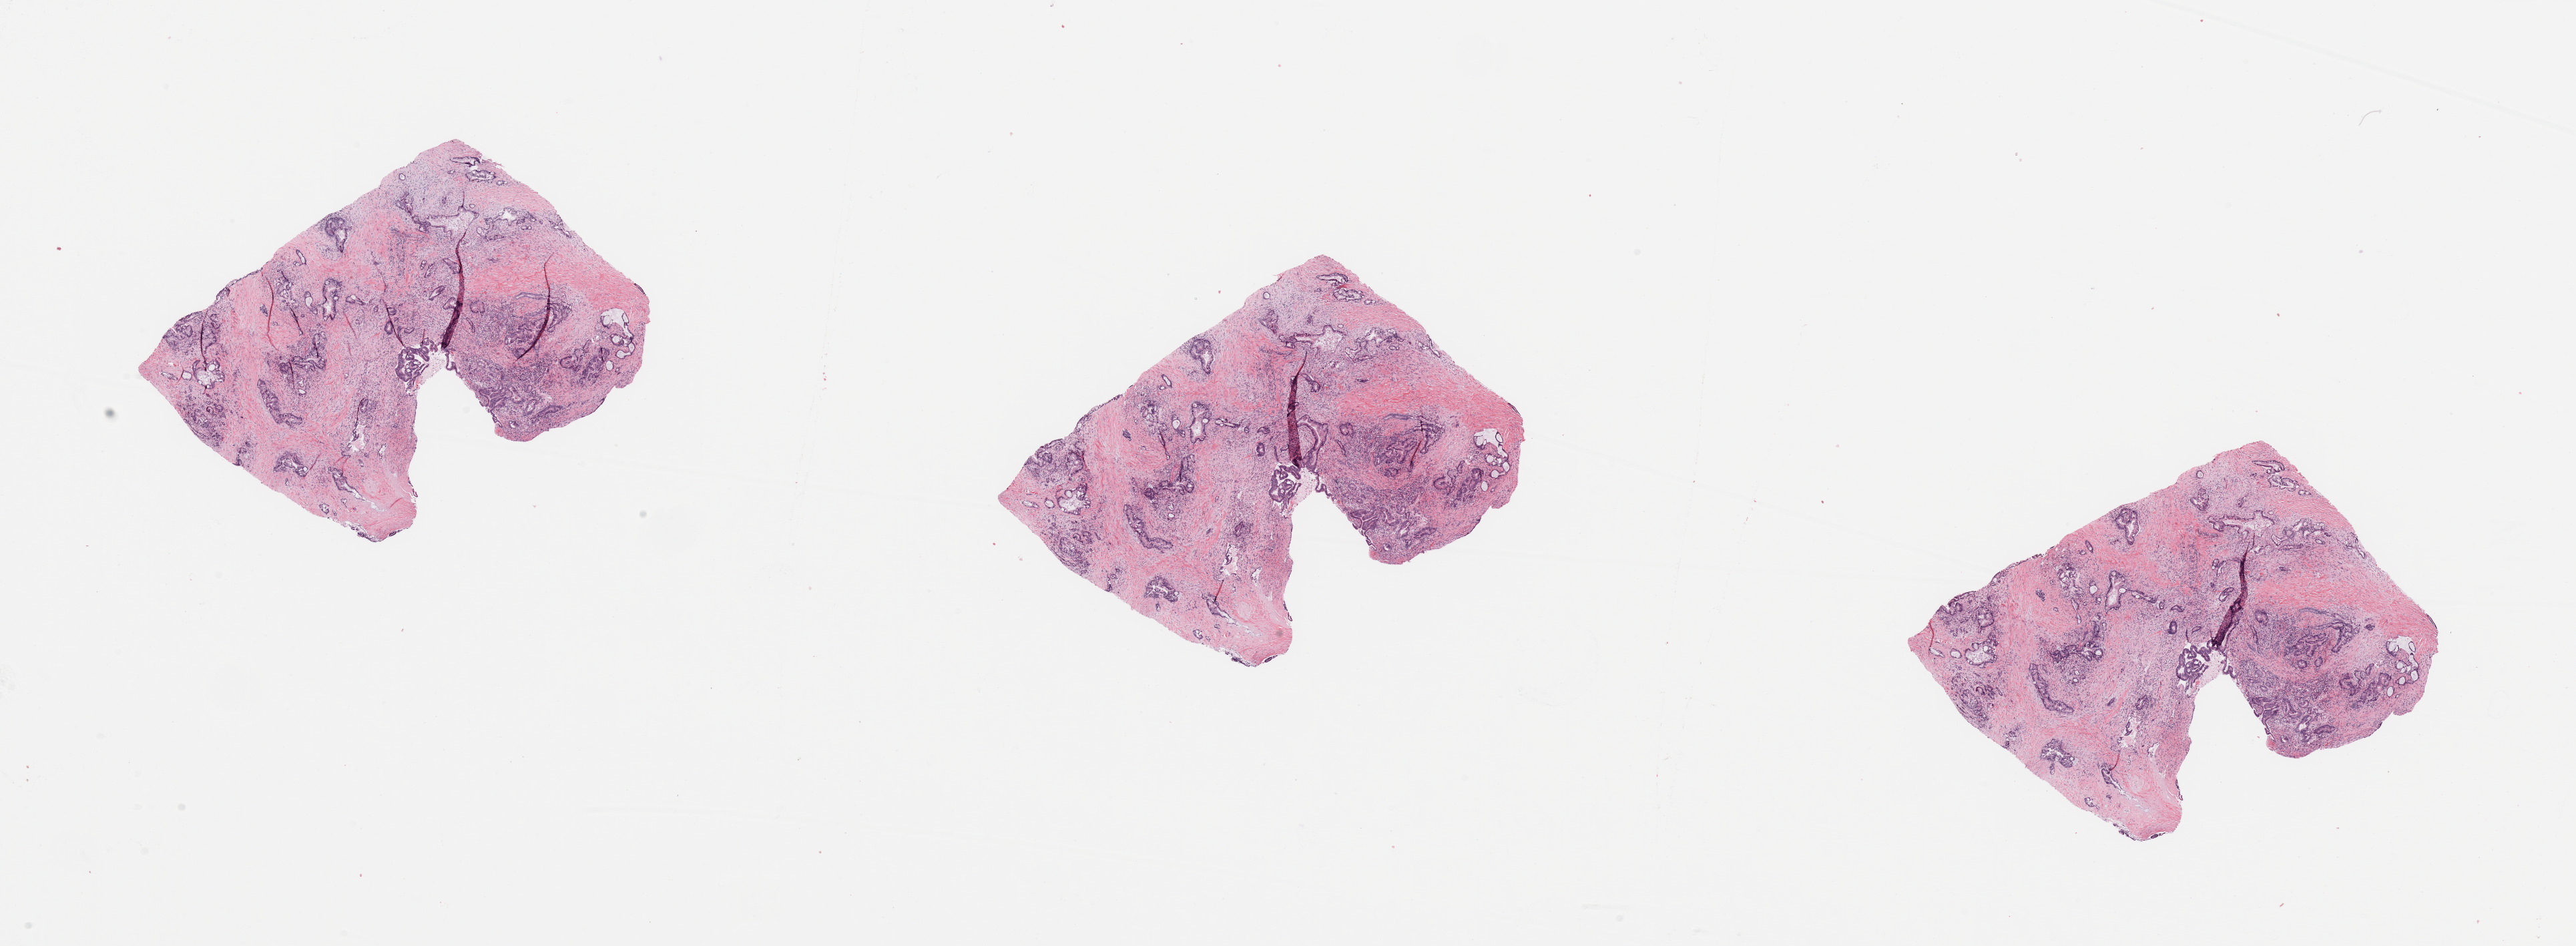
Whole-slide histology image, Hematoxylin and eosin (H&E) stained — low-resolution overview of the scanned area, about 30.5 x 11.2 mm (acquisition: 20x scan); tumour tissue sample, sampled site: pancreas. 34-year-old female patient. Histologic grade: G2 (moderately differentiated). Pathologist review of this section (percent, as recorded): tumour nuclei 80%, necrosis 0%.
Primary tumour site (as recorded): head. Histologic diagnosis: Infiltrating duct carcinoma, NOS. AJCC pathologic stage: IIB.